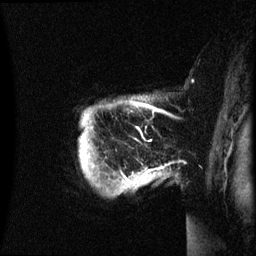
Breast MRI (dynamic contrast-enhanced), one sagittal slice. Slice 55 of 60 in the series (ordered by position). Dynamic contrast-enhanced series, image 2 of 3 at this slice position (ordered by acquisition). 1.5 T. TE 4.2 ms, TR 8.4 ms. 2.4 mm slice thickness. 256 × 256 image matrix. Patient: female, 49 years.
Structures marked on this image (semi-automatically segmented with operator editing):
- analysis volume of interest (the breast-tissue region the enhancement analysis was run in; not a lesion): box from (x=79, y=96) to (x=166, y=195) px
- tumour enhancement mask (voxels above the 70 % enhancement threshold inside the analysis volume of interest): (x=124, y=104)–(x=148, y=179)